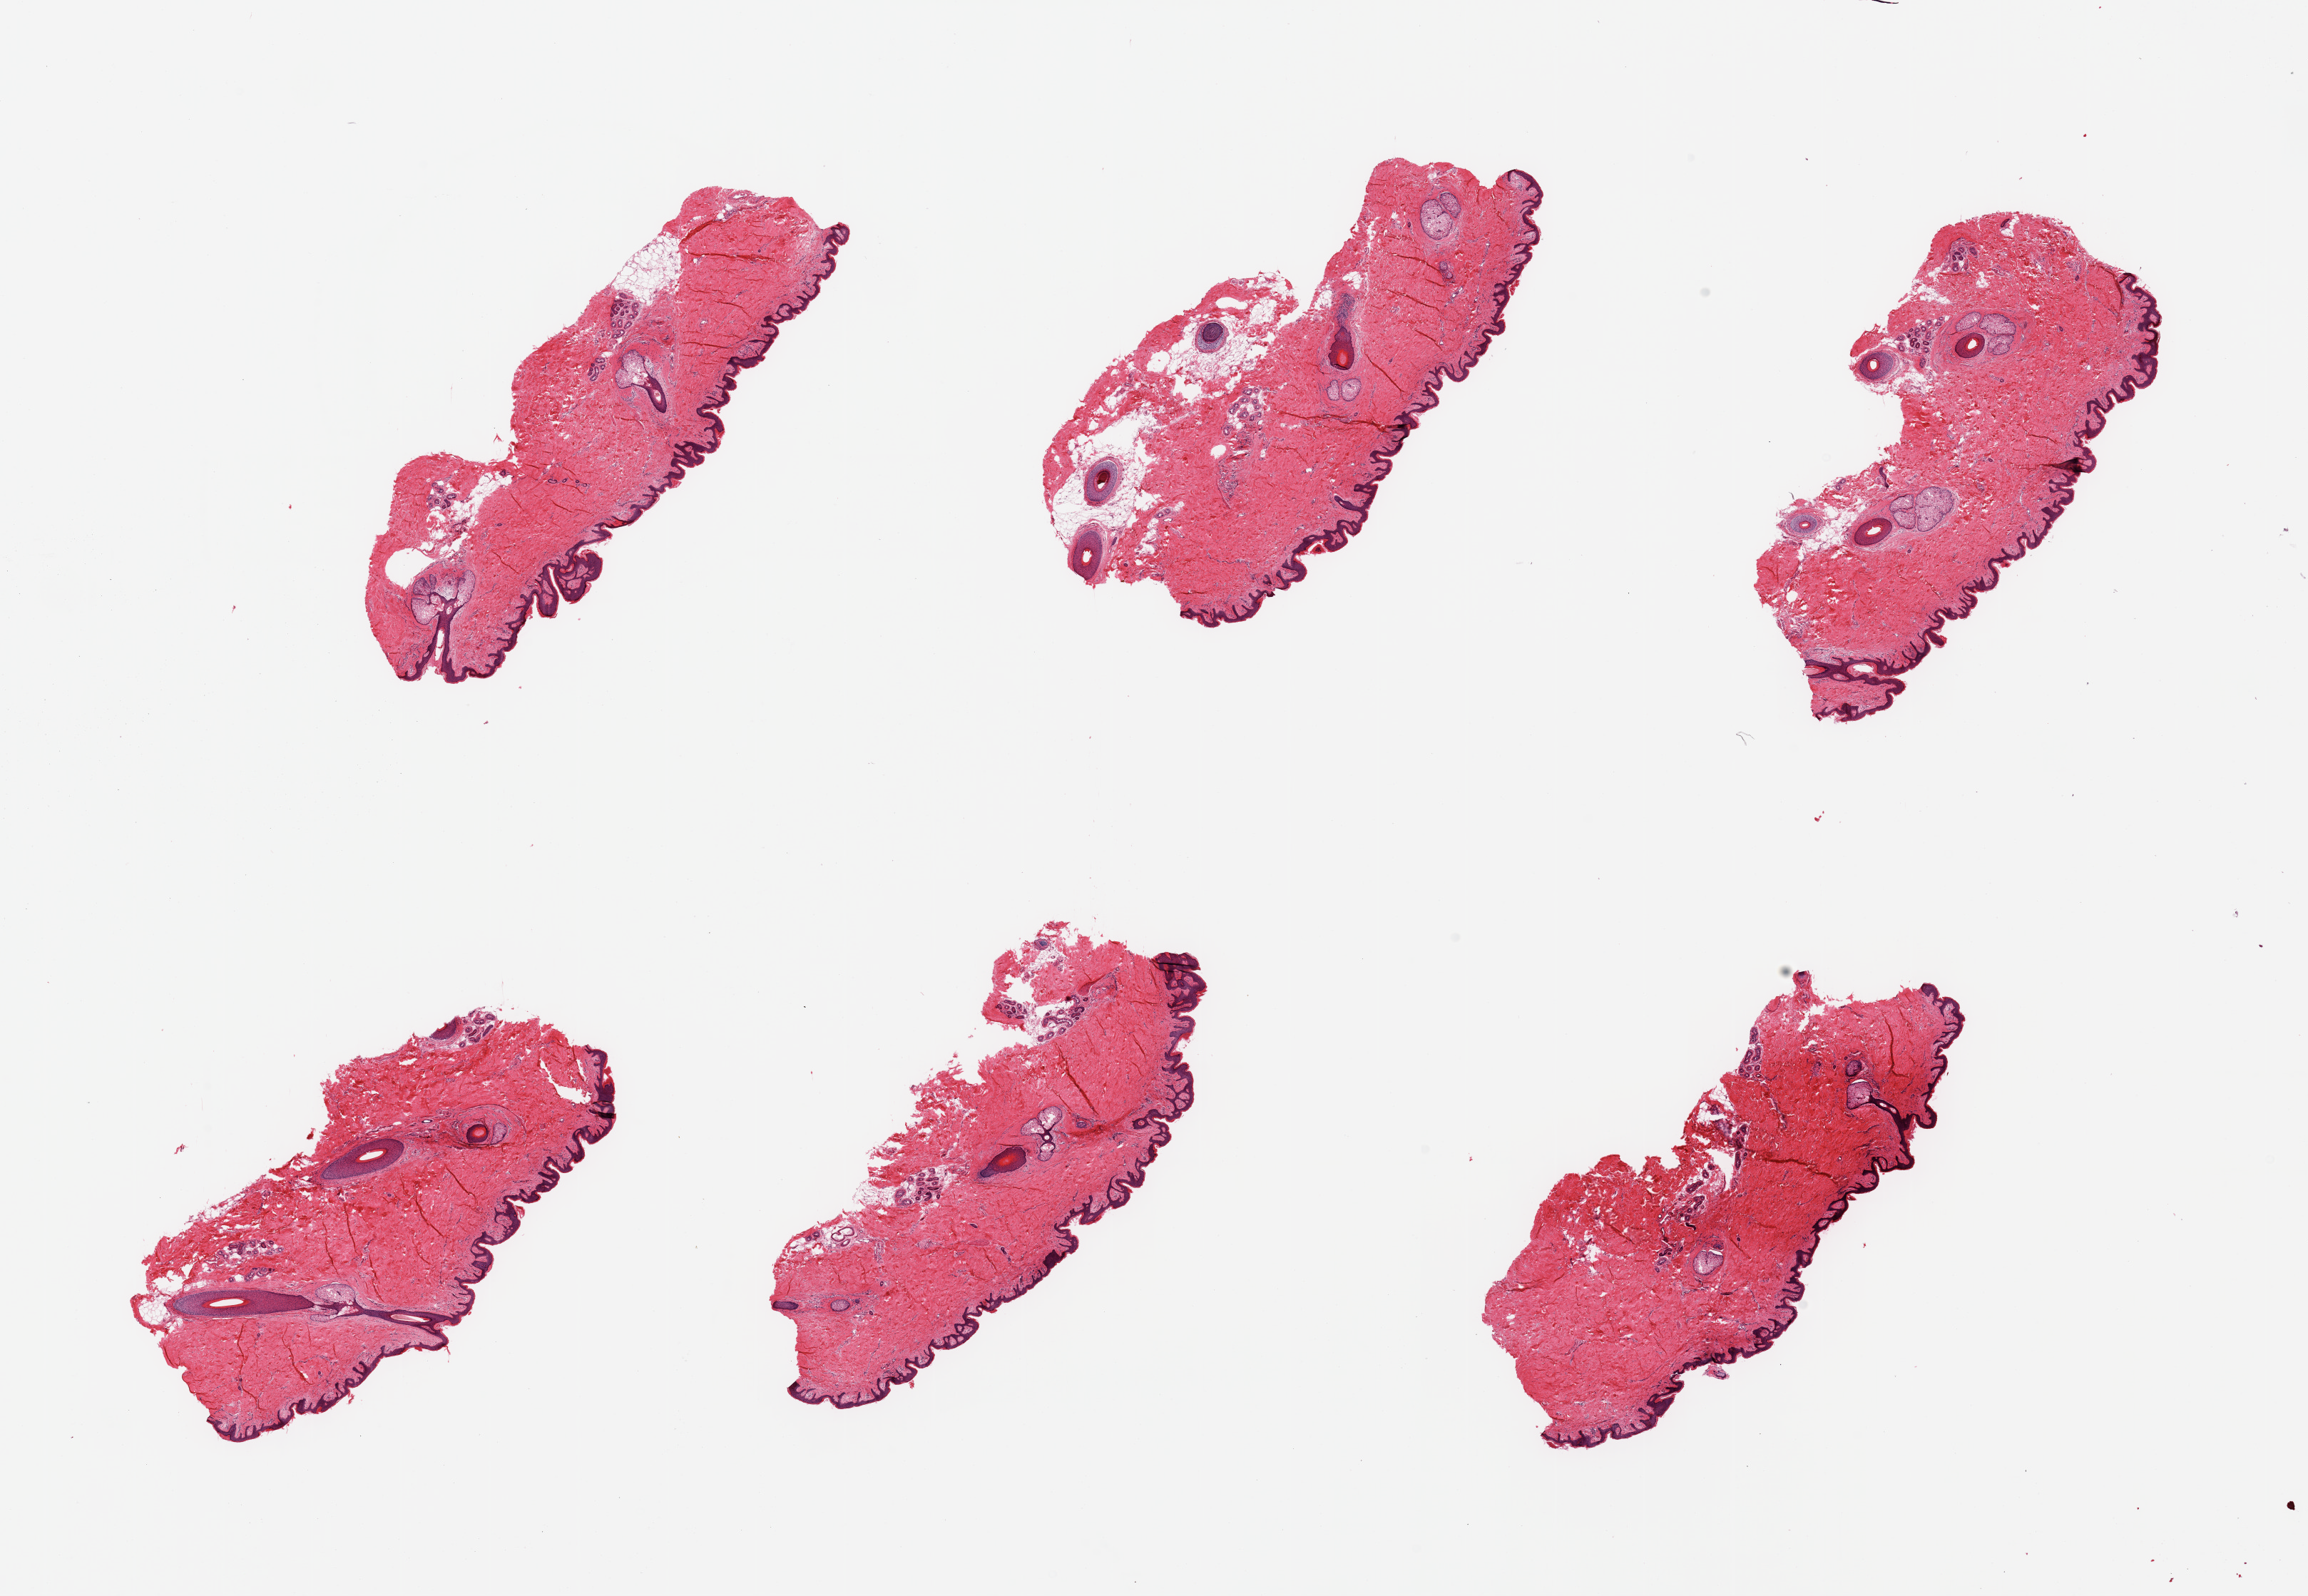
Whole-slide image, hematoxylin and eosin (H&E) stain — whole scanned area (about 25.6 x 17.7 mm, from a 20x scan) shown as a low-resolution overview, PAXgene-fixed paraffin-embedded (PFPE) section, target tissue: skin of suprapubic region, donor tissue sample. Male donor.
Review note (as recorded): 6 pieces, squamous epithelium is ~30-40 microns, trace adherent fat.